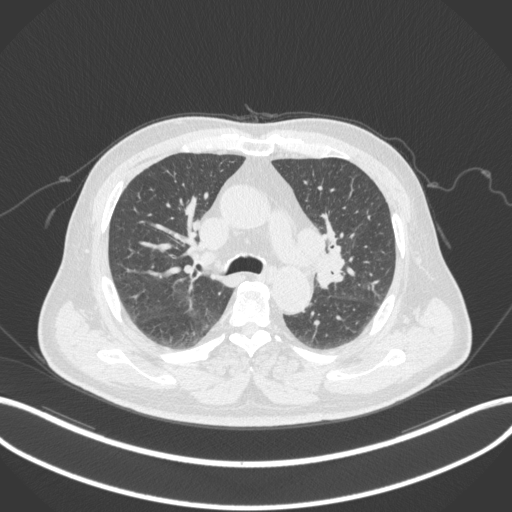
Chest CT, one axial slice; slice 192 of 286 in the series (ordered by position); lung window (W 1500 / L -600 HU); 512 × 512 image matrix. Male patient, age 67 years. Case-level facts recorded for this patient, not image findings: clinical TNM (as recorded): T2a N1 M0; histopathological grade: G3.
Annotated regions visible in this slice (rectangle marked by the reading radiologist):
- lung tumour (recorded histology: adenocarcinoma): box from (x=314, y=243) to (x=347, y=289) px